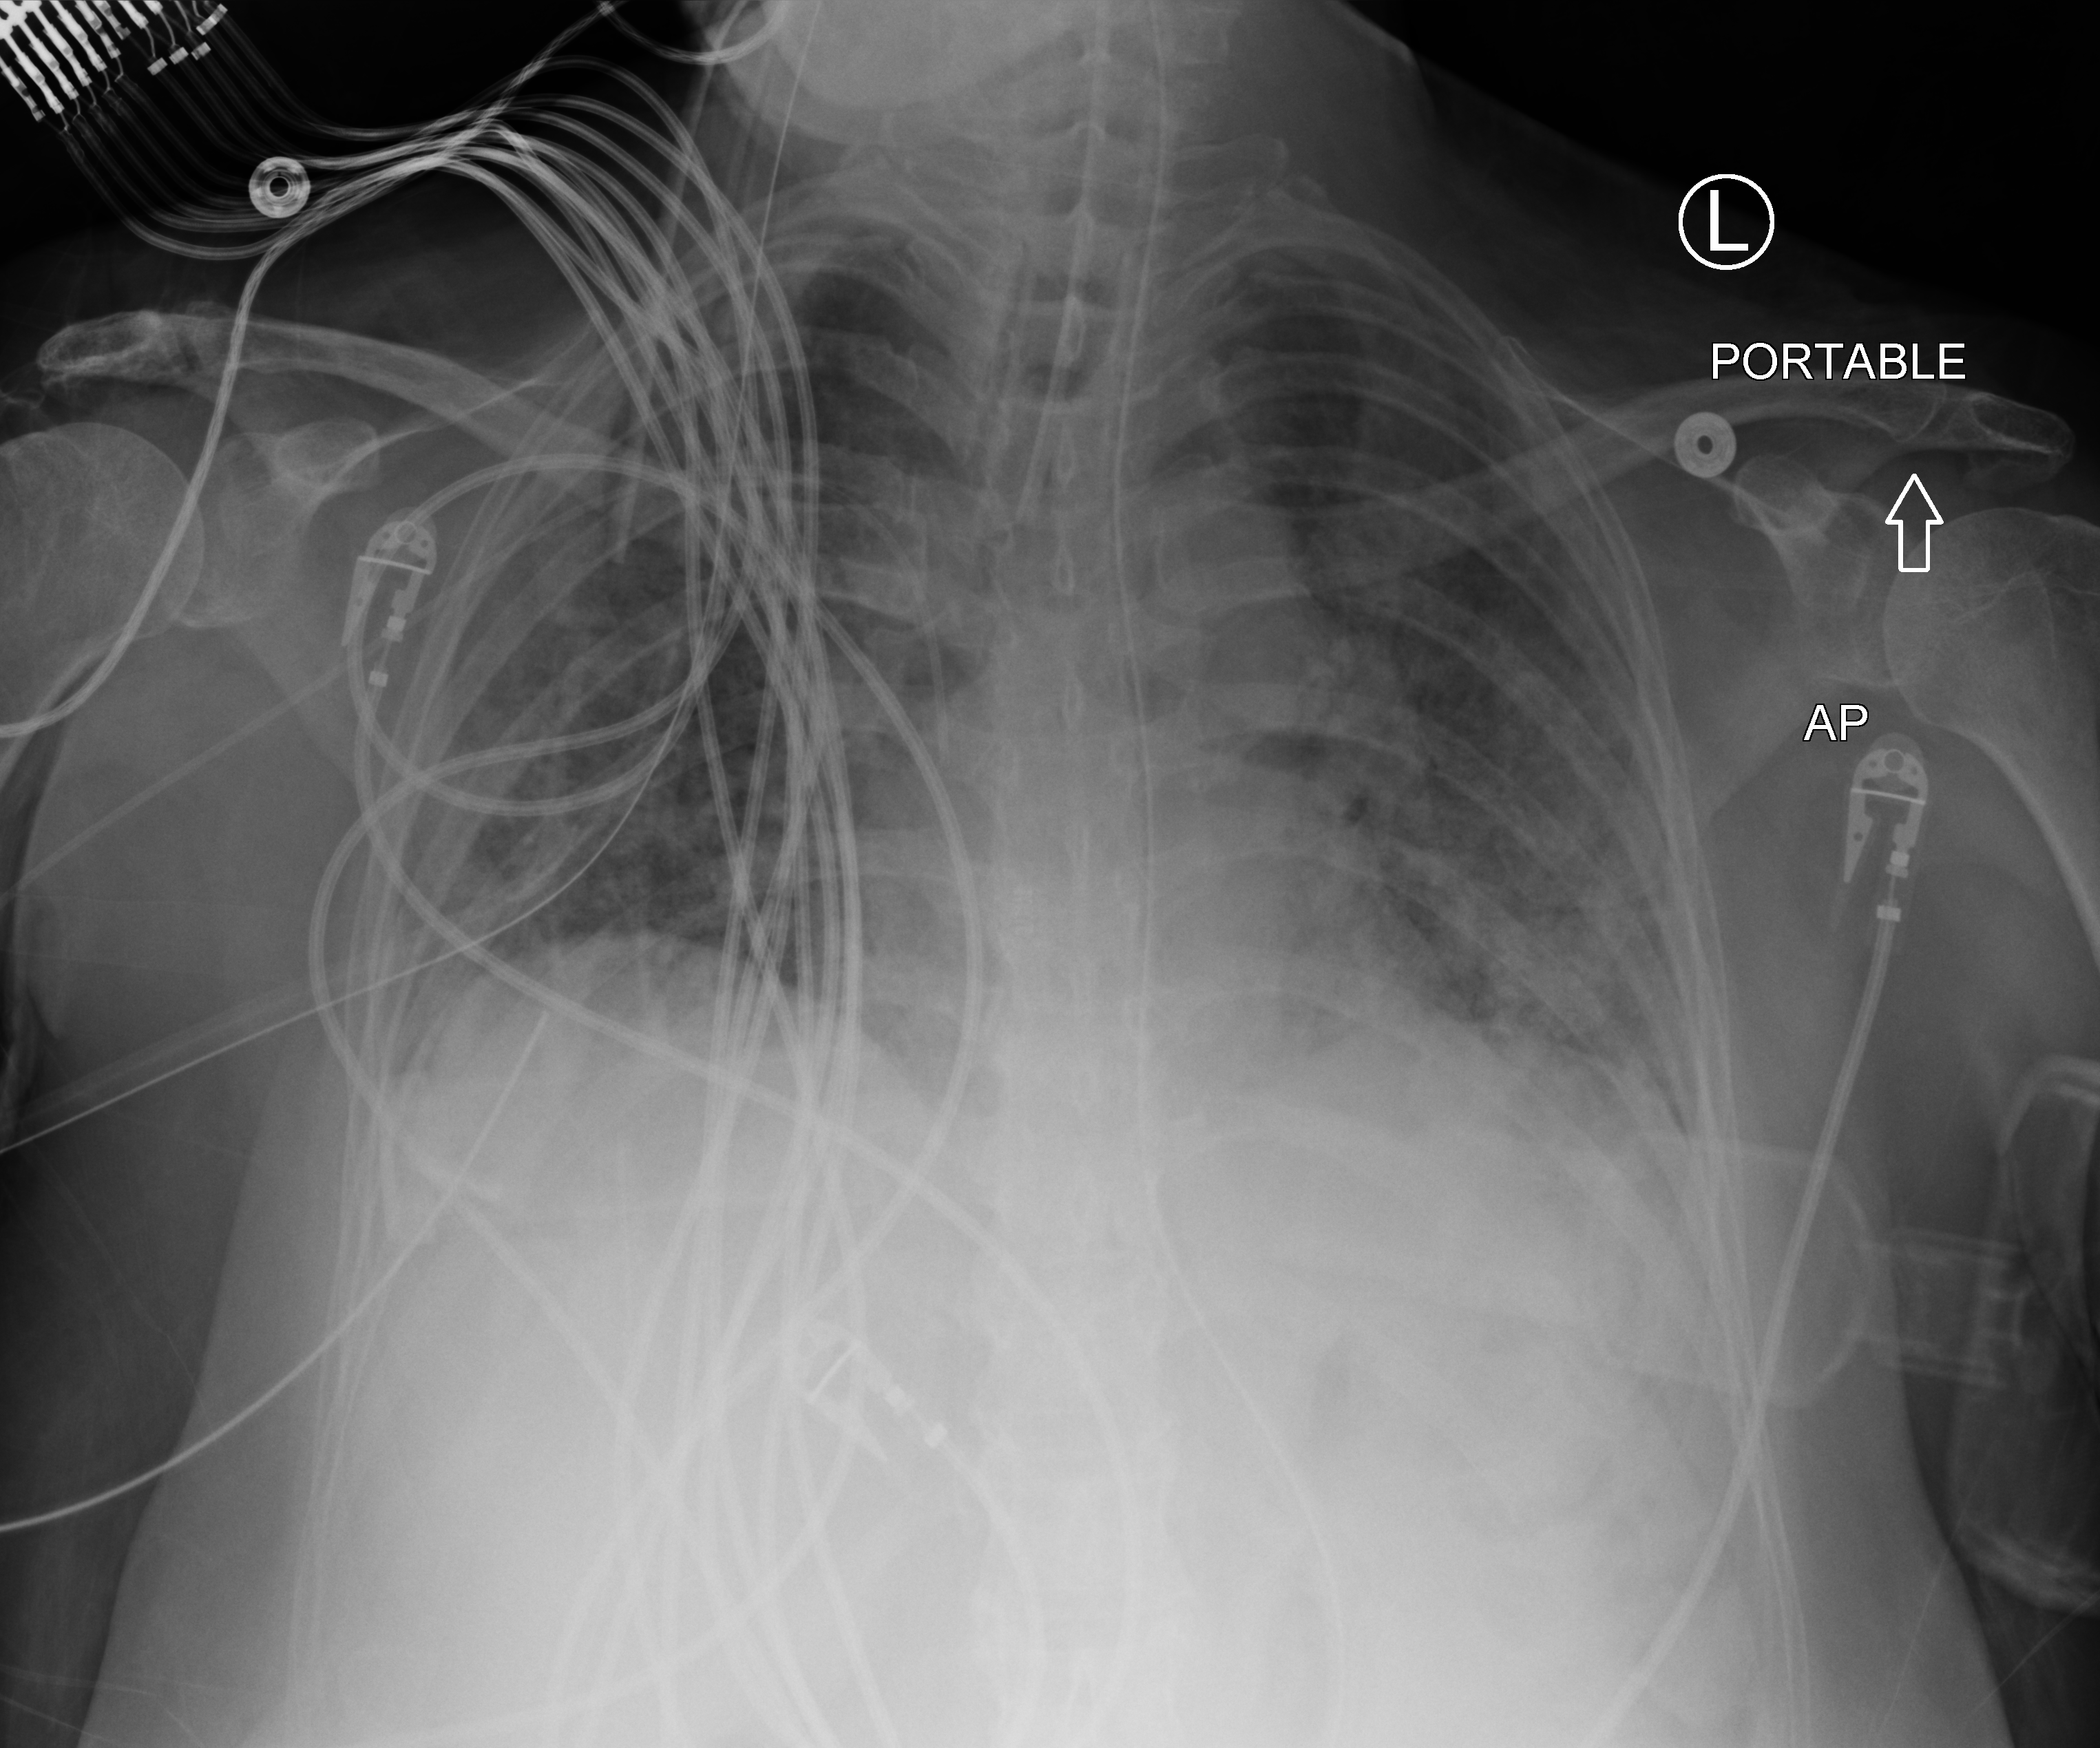
Chest X-ray (portable); anteroposterior (AP) projection. Patient hospitalised with COVID-19; female, aged 60–74 years.
Admission-level facts for this patient (not findings on this image; timing relative to this image not recorded): other chronic lung disease (admission record): no; mechanically ventilated during this hospital stay: yes.